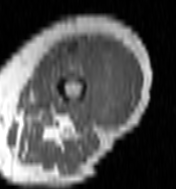
MRI of an extremity soft-tissue mass, one axial slice. Position 40 of 100 along the scan axis. MR volume resampled by the dataset authors to the PET/CT grid (not the native acquisition matrix). 3.27 mm slice thickness. 176 × 189 image matrix. Female patient. Case-level facts recorded for this patient, not image findings: histological type: undifferentiated – high grade; grade: high; site of the primary tumour: left thigh.
Outlined on this slice (expert contour drawn on MRI and transferred to this co-registered scan by the dataset authors):
- gross tumour volume including surrounding oedema: bounding box (x1, y1, x2, y2) in pixels: (60, 45, 134, 126)
- gross tumour volume (mass): (78, 45, 131, 126)